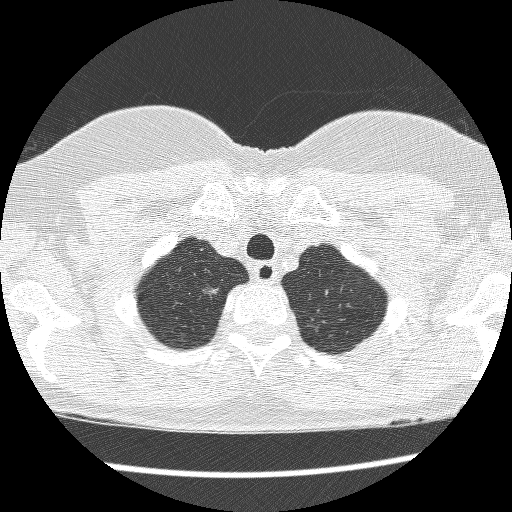
Axial slice from a low-dose chest CT screening exam, first (baseline) screen, lung window (W 1500 / L -600 HU), lung (sharp) reconstruction kernel (BONE), 120 kVp, 512 × 512 image matrix. Female, age 61 years at enrolment.
- Expert reader's lesion annotation, box from (x=198, y=281) to (x=225, y=304) px.
- Screening reader's record for this exam (one nodule recorded; not confirmed to be the boxed lesion): non-calcified nodule or mass ≥4 mm, right upper lobe, 7 × 6 mm, poorly defined margins, mixed attenuation.
- Participant outcome: lung cancer diagnosed 403 days after this screen (after the second annual screen) — adenocarcinoma, NOS, right upper lobe, poorly differentiated (G3), 12 mm at pathology.